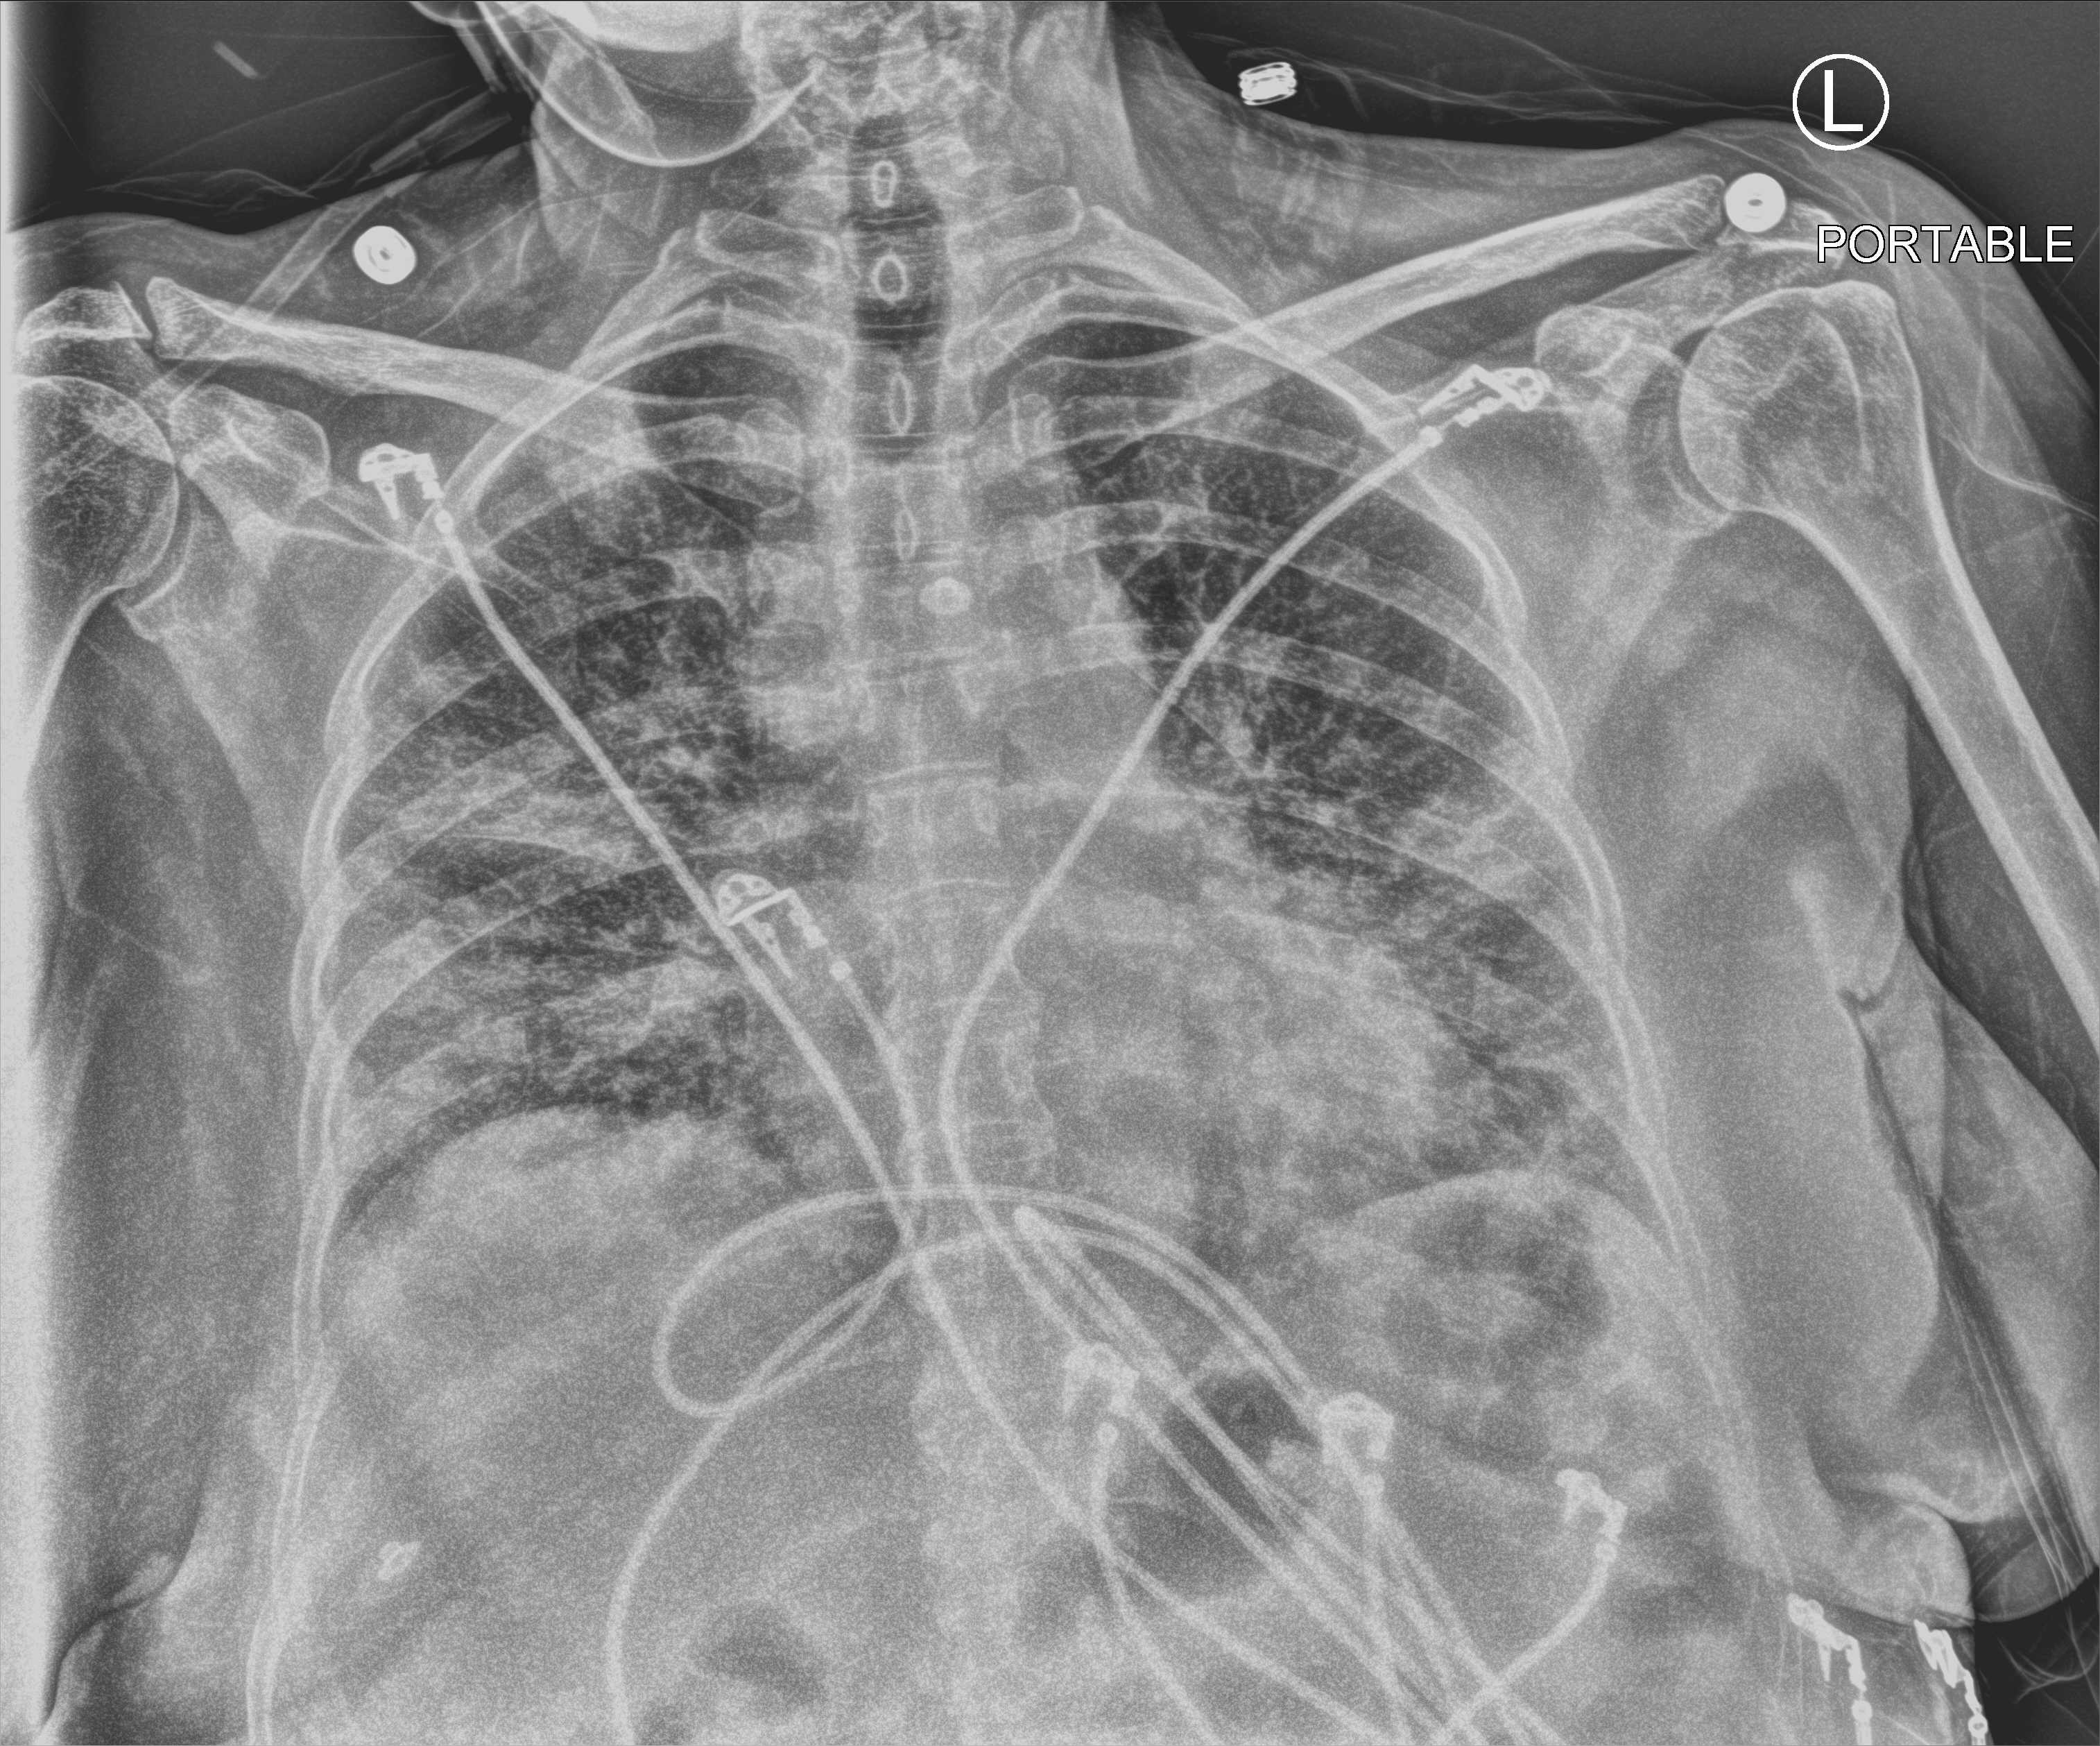
Chest X-ray (portable), anteroposterior (AP) projection. Female patient hospitalised with COVID-19, age 60–74 years.
Hospital-stay facts (about this admission, not read from this image; timing relative to this image not recorded):
- mechanically ventilated during this hospital stay: yes
- admitted to intensive care during this hospital stay: yes
- length of hospital stay: 43 days